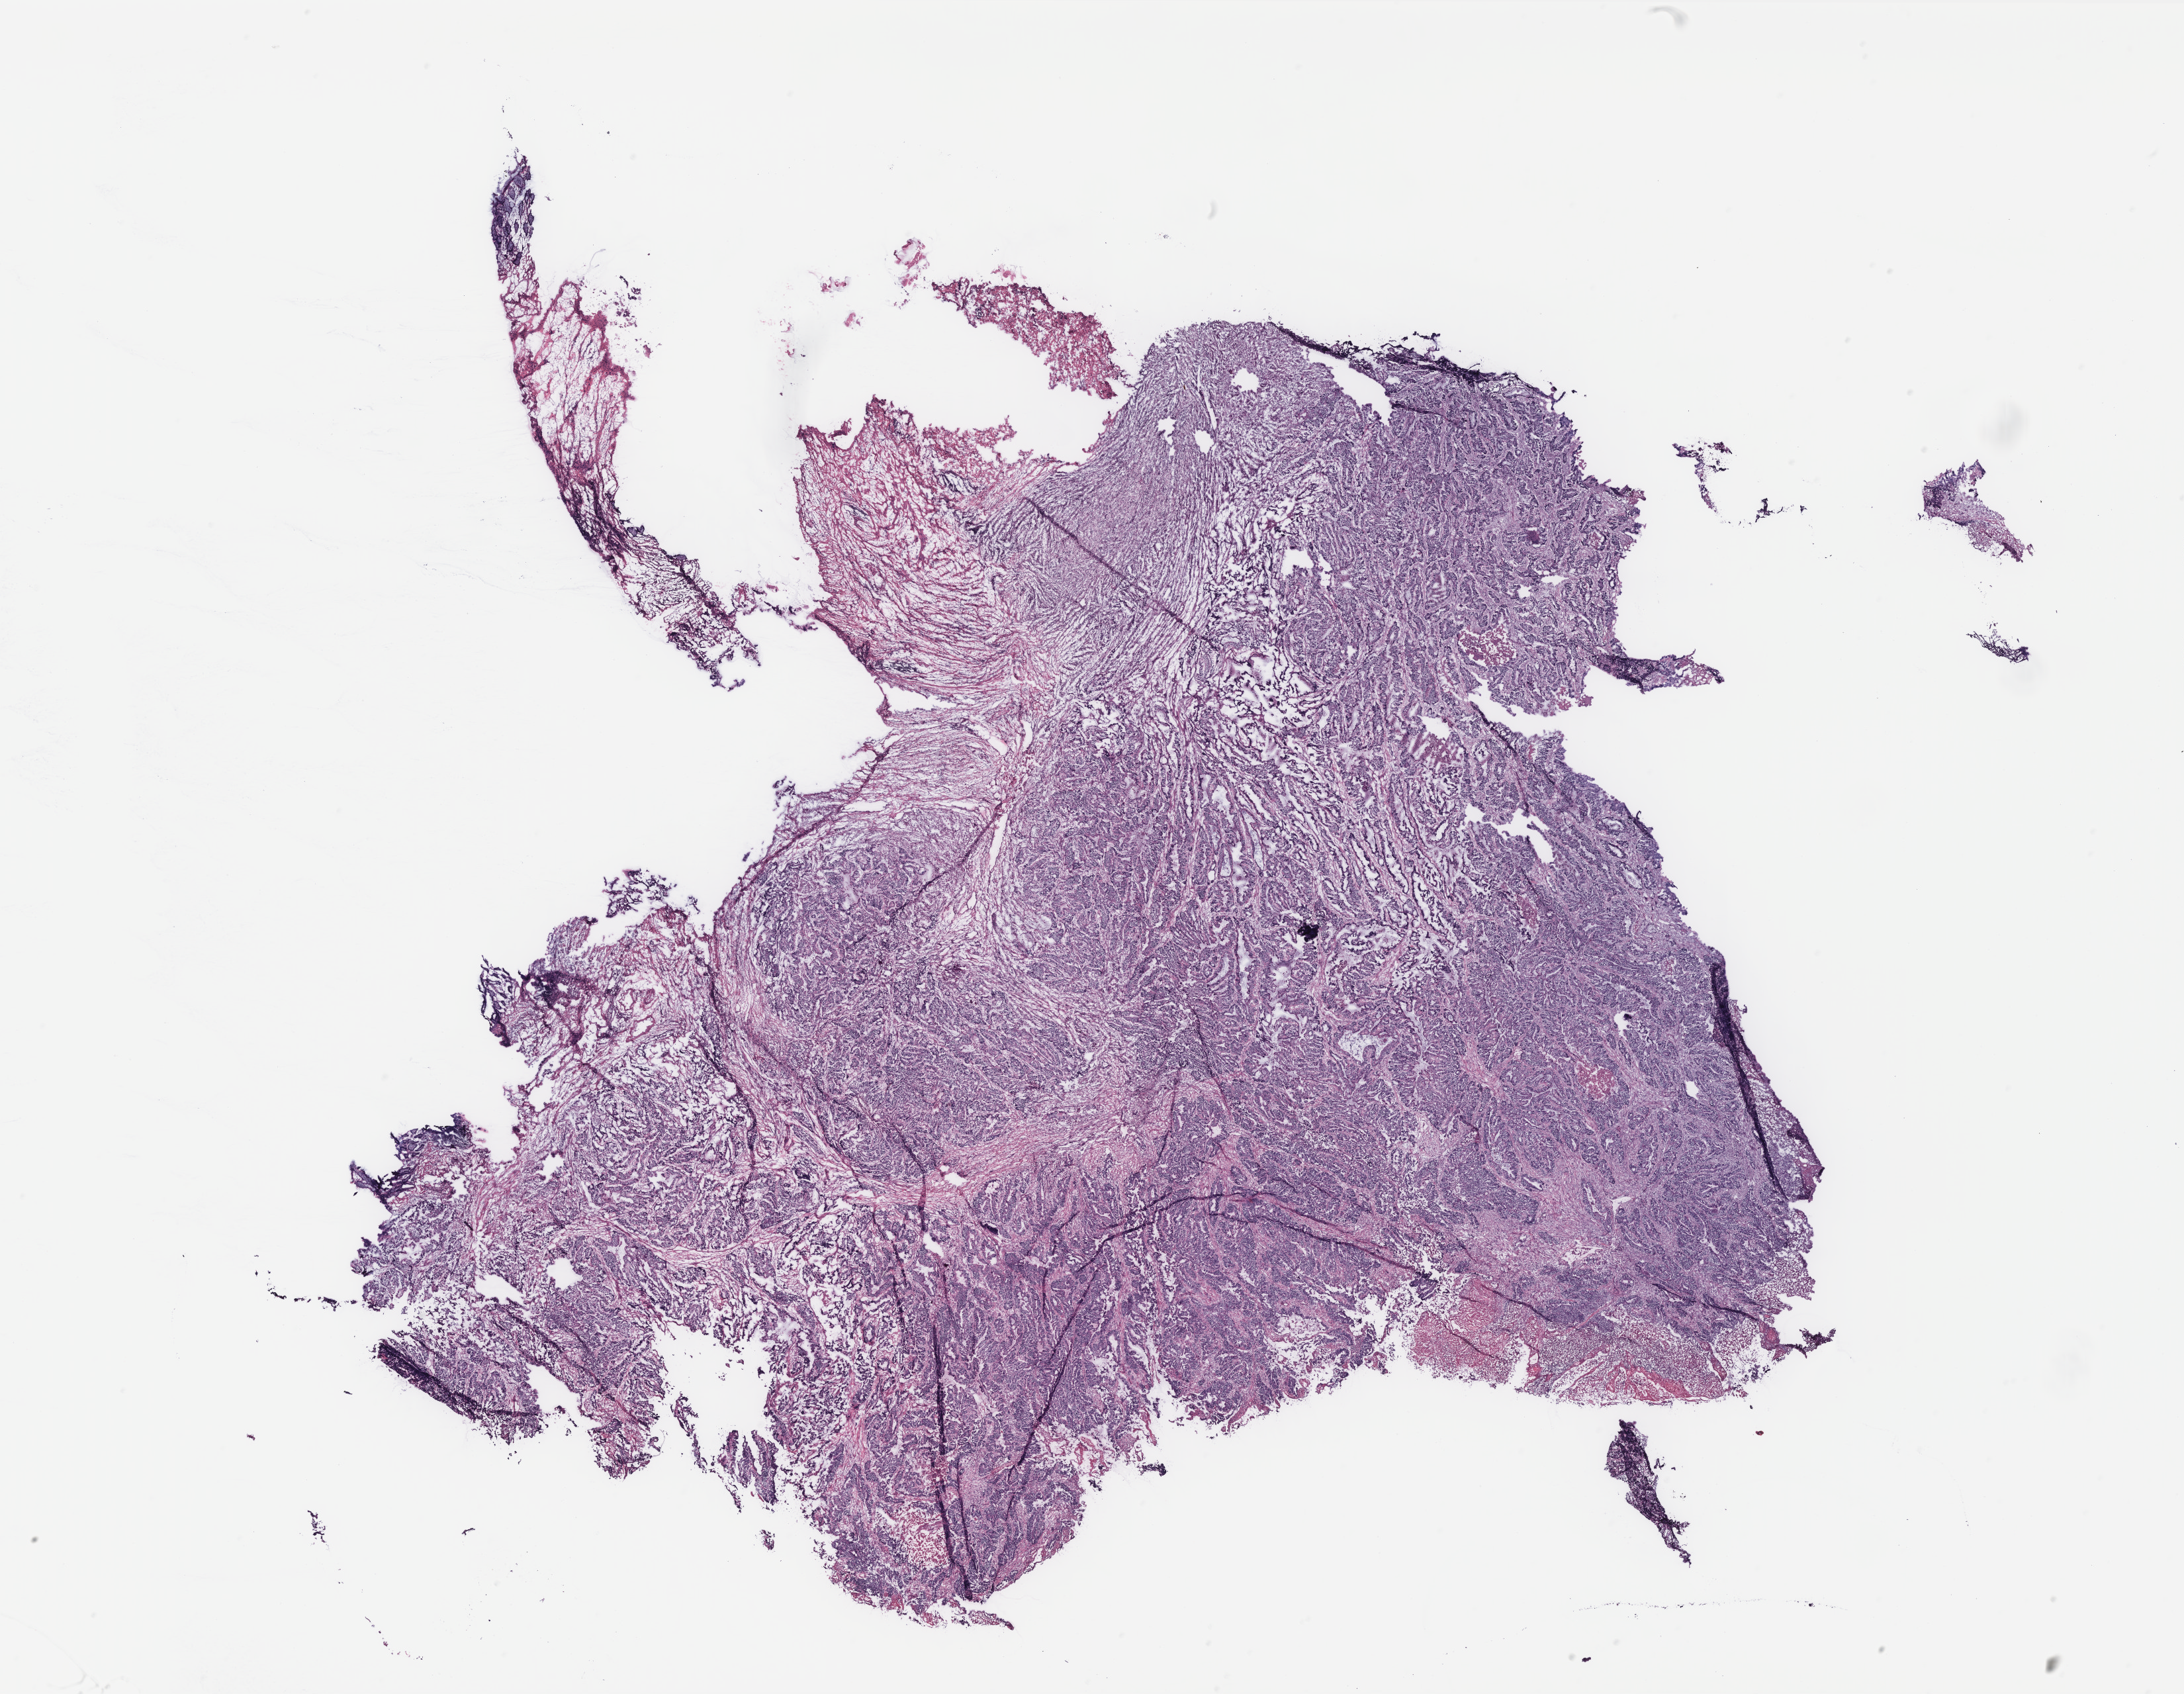
Whole-slide histology image, H&E-stained — low-resolution overview of the scanned area, about 26.4 x 20.5 mm, colon, tissue type not recorded.
Patient diagnosis (cohort enrolment): colon cancer (colon).